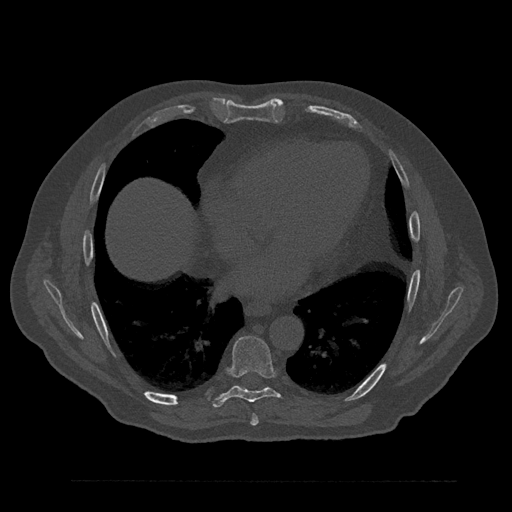
CT including the spine, one axial slice; position 453 of 797 along the scan axis; reconstruction kernel Br40s/3; 120 kVp; bone window (W 1800 / L 400 HU); 512 × 512 image matrix. Male patient, age 61 years. From the clinical record (not read from this slice): primary cancer: prostate.
Annotated regions visible in this slice (semi-automatically segmented with operator editing):
- T7 vertebra: bounding box [x1, y1, x2, y2] px = [250, 415, 259, 426]
- T8 vertebra: [211, 335, 281, 408]